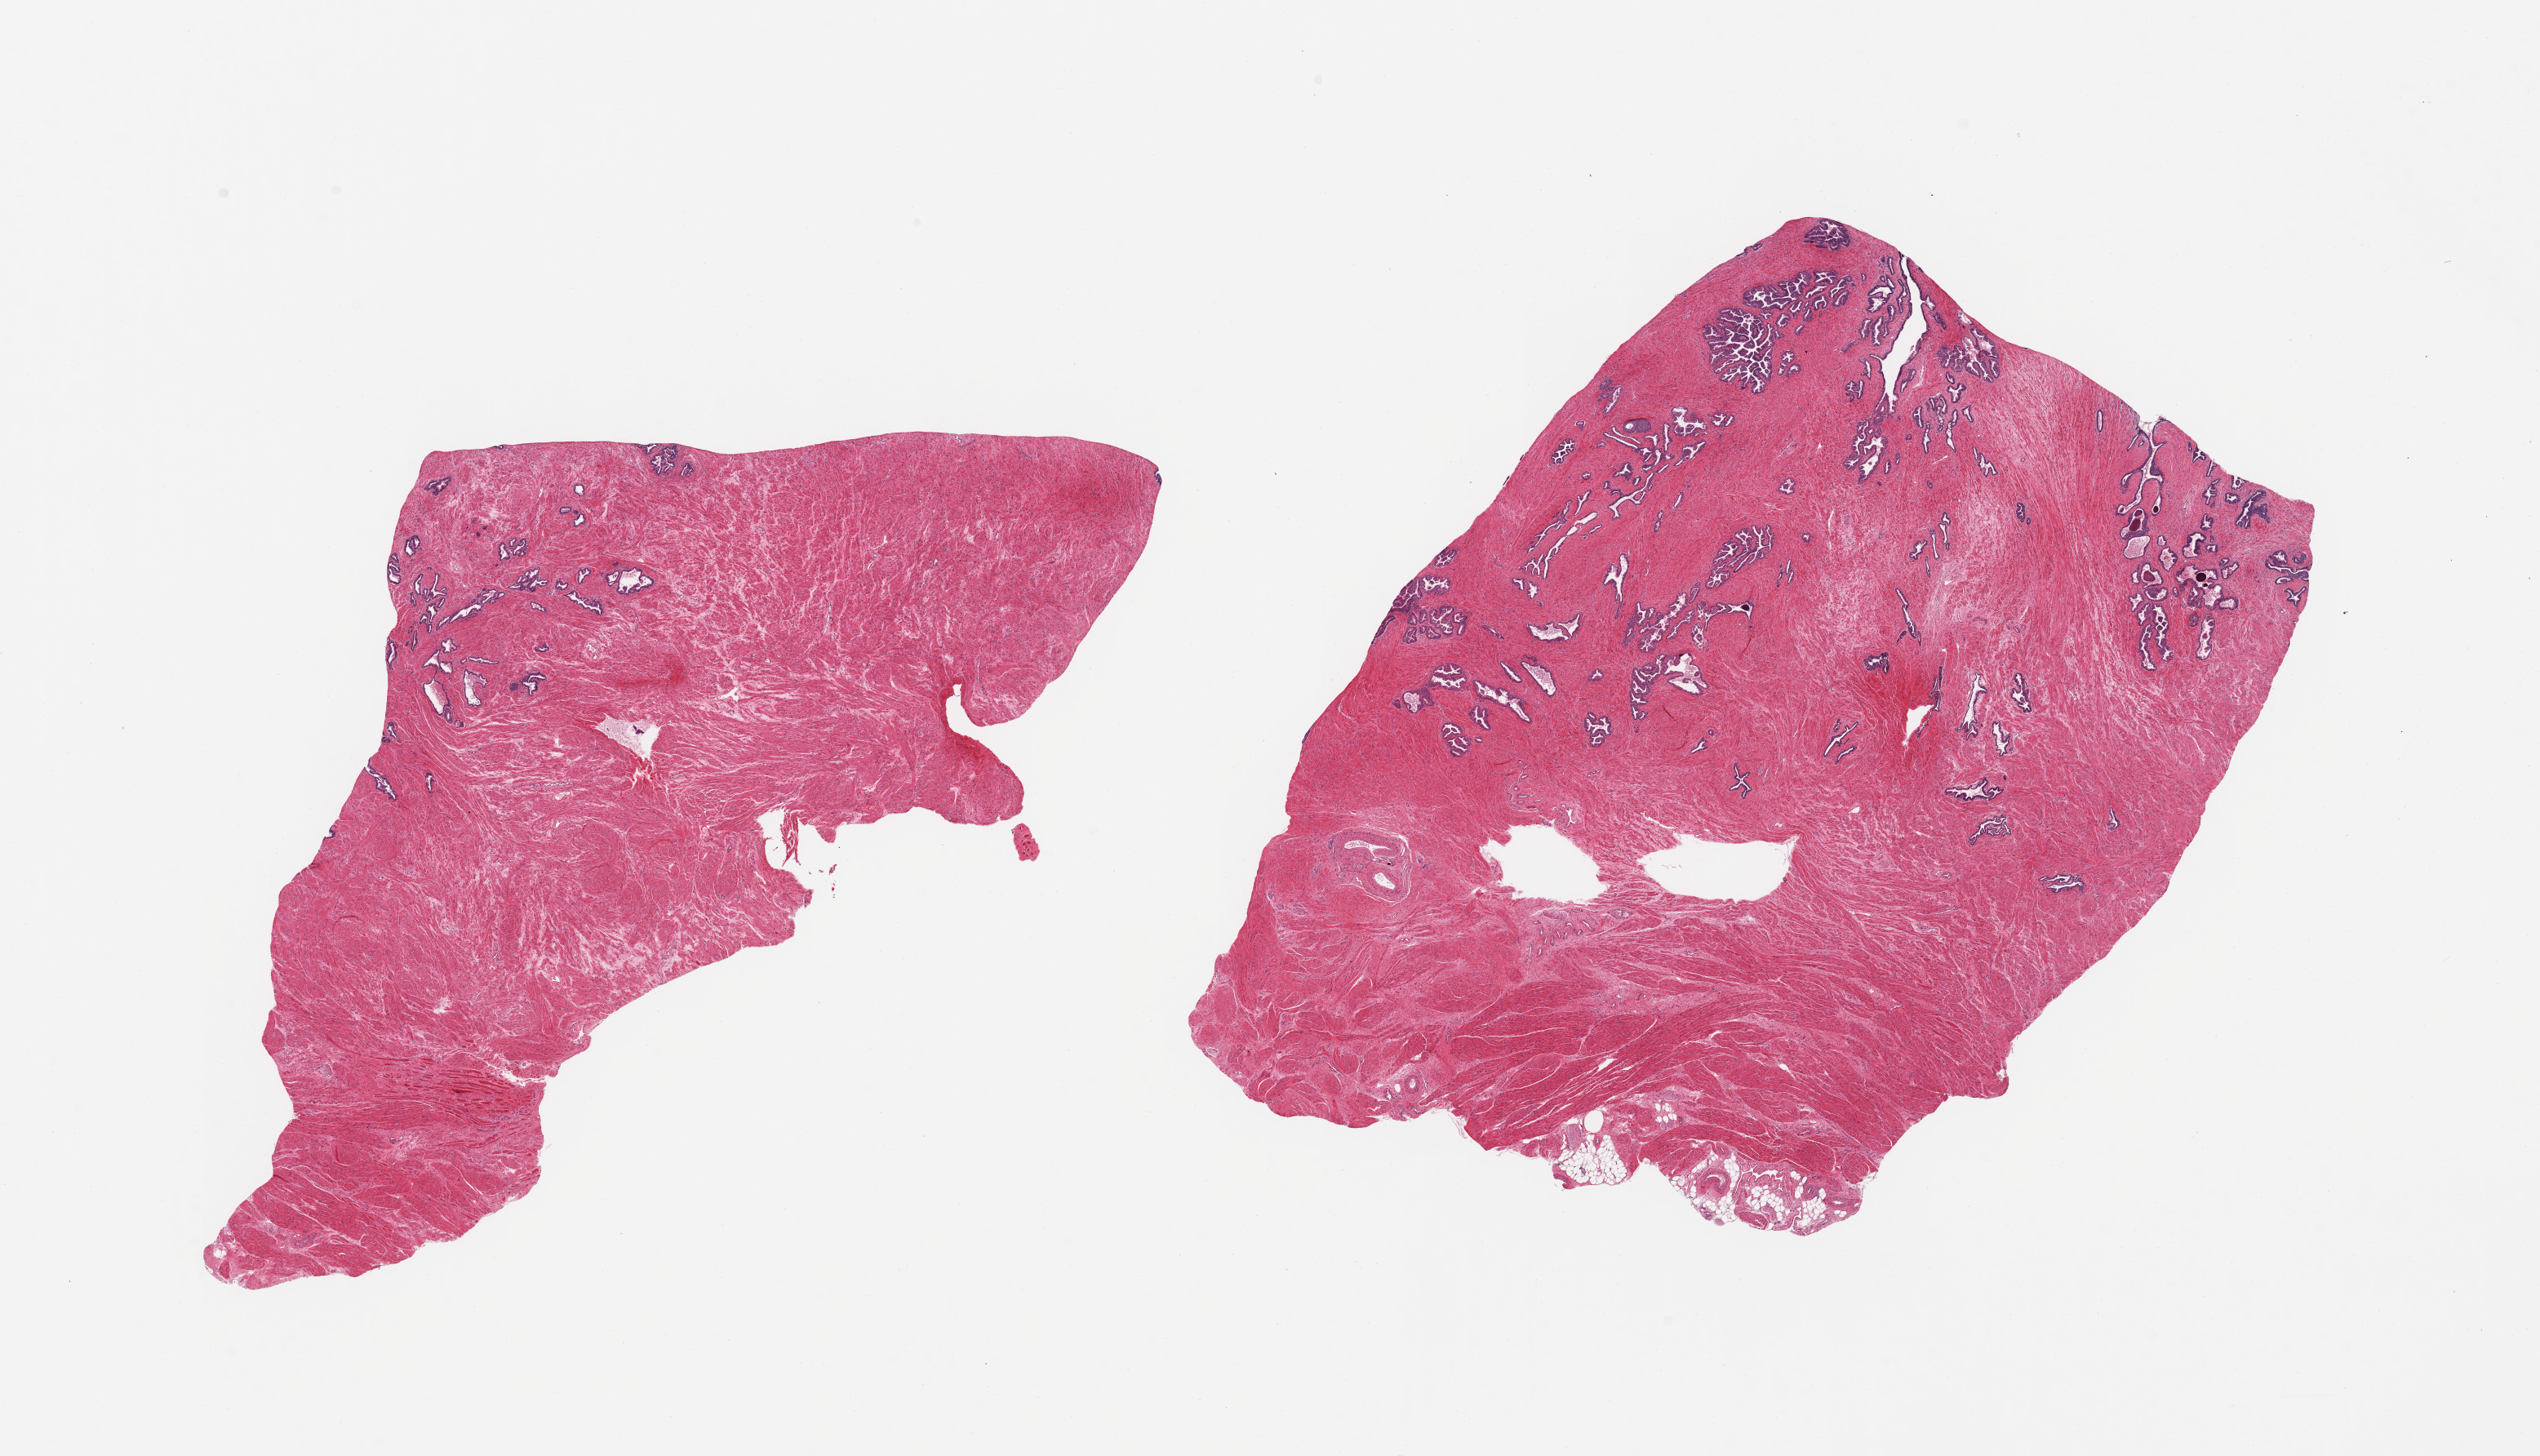
Hematoxylin and eosin (H&E) whole-slide image, brightfield, a low-resolution overview of the entire scanned area, about 24.6 x 14.1 mm, PAXgene-fixed, paraffin-embedded tissue, target tissue: prostate, tissue donor sample. Male donor.
Review note (as recorded): 2 pieces, mainly stroma, no abnormalitites.